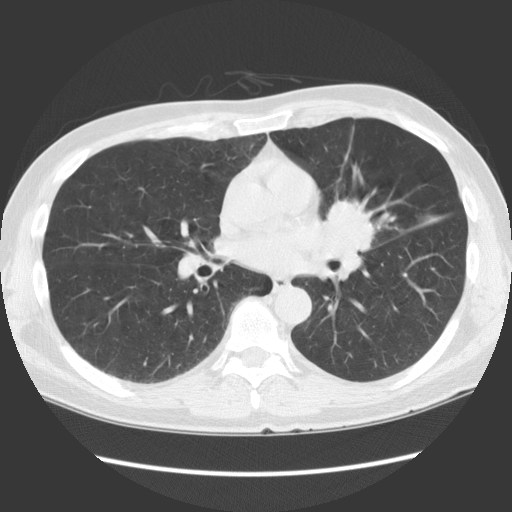
Axial slice from a low-dose chest CT screening exam, first (baseline) screen, lung window (W 1500 / L -600 HU), slice 68 of 136 in the series. Male participant, aged 61 years at enrolment.
Expert reader's lesion annotation, box from (x=300, y=187) to (x=396, y=287) px. The exam's reader record, not a measurement of the box and not confirmed to be the same lesion: non-calcified nodule or mass ≥4 mm, lingula, 35 × 35 mm, spiculated (stellate) margins, soft tissue attenuation. Official screen result: positive, change unspecified: nodule(s) >= 4 mm or enlarging nodule(s), mass(es), or other non-specific abnormalities suspicious for lung cancer. Participant outcome: lung cancer diagnosed 58 days after this screen — squamous cell carcinoma, NOS, left hilum, left main stem bronchus, poorly differentiated (G3), stage IA (AJCC 6th edition), 40 mm at pathology.